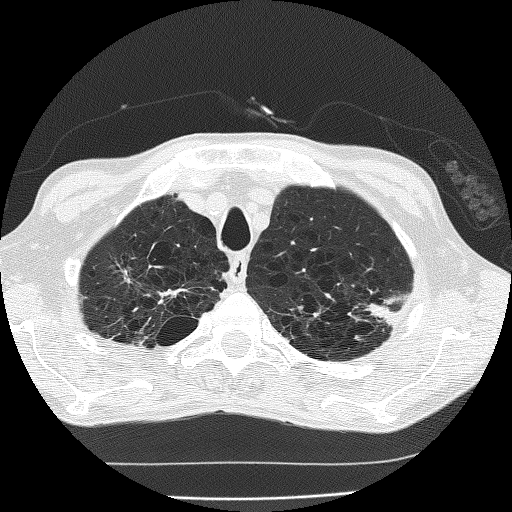
Low-dose screening chest CT, one axial slice; slice 157 of 185 in the series (ordered by position); reconstruction kernel FC51; 120 kVp; lung window (W 1500 / L -600 HU); 2 mm slice thickness; 512 × 512 image matrix, field of view 320 × 320 mm.
Outlined on this slice (outlined manually by an expert reader):
- lesion 1 (tumor, upper lobe of left lung): box from (x=367, y=304) to (x=397, y=324) px